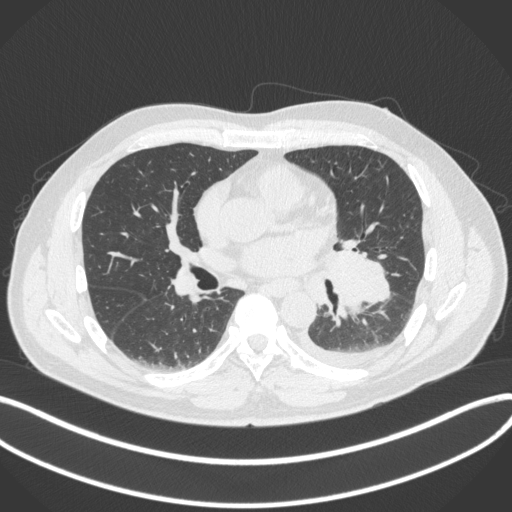
Chest CT, one axial slice. Position 184 of 350 along the scan axis. 120 kVp. Lung window (W 1500 / L -600 HU). 1 mm slice thickness. 512 × 512 image matrix, field of view 400 × 400 mm. Male patient, age 58 years. Case-level facts recorded for this patient, not image findings: clinical TNM (as recorded): T3 N1 M1b; histopathological grade: G3.
Annotated regions visible in this slice (rectangle marked by the reading radiologist):
- lung tumour (recorded histology: small cell carcinoma): box from (x=326, y=240) to (x=394, y=322) px